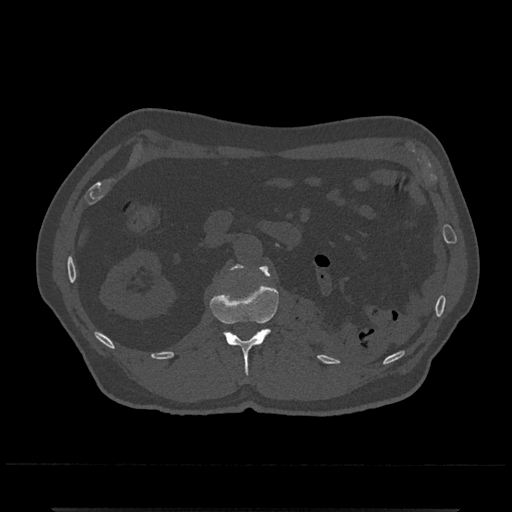
CT including the spine, one axial slice. Slice 349 of 797 in the series (ordered by position). 120 kVp. Bone window (W 1800 / L 400 HU). 0.5 mm slice thickness. 512 × 512 image matrix, field of view 393 × 393 mm. Patient: male, 67 years. Case-level facts recorded for this patient, not image findings: primary cancer: prostate.
Annotated regions visible in this slice (semi-automatic segmentation, software-assisted and operator-edited):
- L1 vertebra: bounding box <210,264,279,376> (left, top, right, bottom; pixels)